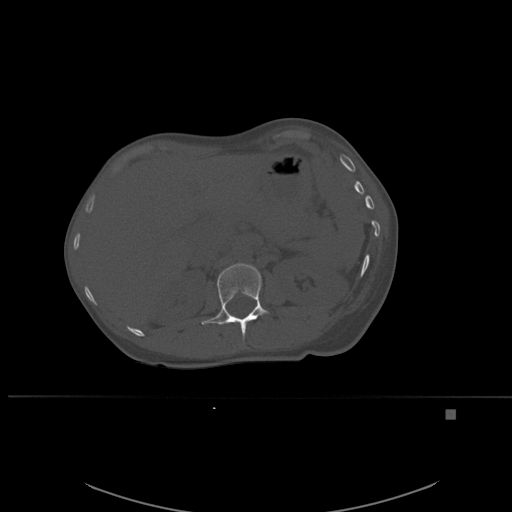
CT including the spine, one axial slice; slice 260 of 537 in the series (ordered by position); bone window (W 1800 / L 400 HU); 1.5 mm slice thickness; 512 × 512 image matrix. Patient: female, 45 years. Case-level facts recorded for this patient, not image findings: primary cancer: lung.
Annotated regions visible in this slice (semi-automatic segmentation, software-assisted and operator-edited):
- L1 vertebra: bounding box [x1, y1, x2, y2] px = [201, 263, 270, 341]